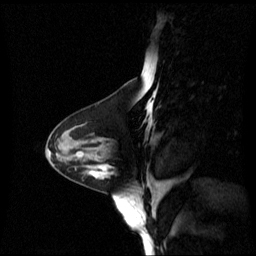
Breast MRI (dynamic contrast-enhanced), one sagittal slice; slice 25 of 60 in the series (ordered by position); dynamic contrast-enhanced series, image 2 of 3 at this slice position (ordered by acquisition); 1.5 T; TE 4.2 ms, TR 8.4 ms; 2.4 mm slice thickness; 256 × 256 image matrix. Female patient, age 44 years. From the clinical record (not read from this slice): setting: breast cancer imaged before/during neoadjuvant chemotherapy; receptor status: triple-negative.
Annotated regions visible in this slice (semi-automatically segmented with operator editing):
- analysis volume of interest (the breast-tissue region the enhancement analysis was run in; not a lesion): bounding box [x1, y1, x2, y2] px = [79, 148, 132, 190]
- tumour enhancement mask (voxels above the 70 % enhancement threshold inside the analysis volume of interest): [93, 168, 107, 177]